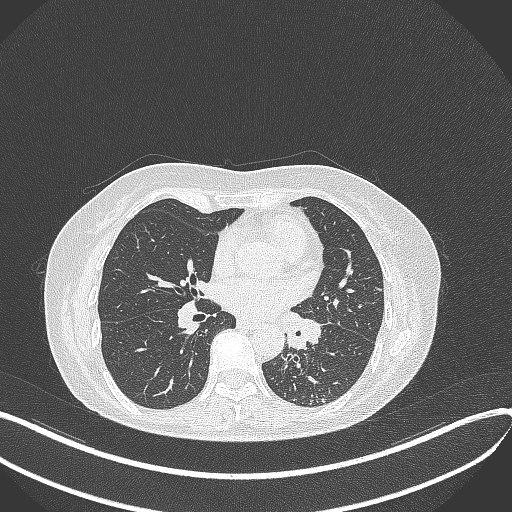
Chest CT, one axial slice. Slice 200 of 429 in the series (ordered by position). Reconstruction kernel B70f. Lung window (W 1500 / L -600 HU). 512 × 512 image matrix, field of view 400 × 400 mm. Patient: female, 63 years. From the clinical record (not read from this slice): clinical TNM (as recorded): T1b N0 M0; histopathological grade: G2-3.
Outlined on this slice (bounding box drawn by a radiologist):
- lung tumour (recorded histology: adenocarcinoma): box from (x=281, y=310) to (x=325, y=349) px